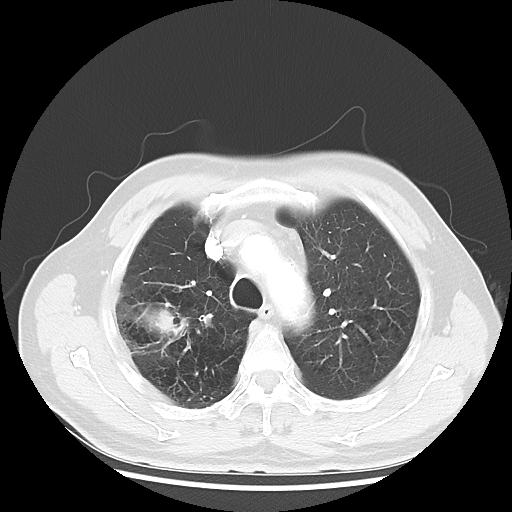
Chest CT, one axial slice; position 38 of 50 along the scan axis; 120 kVp; lung window (W 1500 / L -600 HU); 5 mm slice thickness; 512 × 512 image matrix, field of view 360 × 360 mm. Patient: male, 69 years. Case-level facts recorded for this patient, not image findings: clinical TNM (as recorded): T3 N0 M0; histopathological grade: G3.
Structures marked on this image (bounding box drawn by a radiologist):
- lung tumour (recorded histology: adenocarcinoma): bounding box <115,295,196,351> (left, top, right, bottom; pixels)